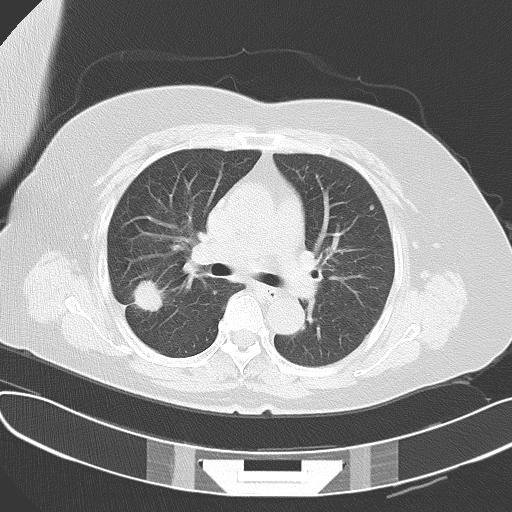
Chest CT, one axial slice; position 43 of 61 along the scan axis; 120 kVp; lung window (W 1500 / L -600 HU); 512 × 512 image matrix, field of view 367 × 367 mm. Patient: female, 63 years. Case-level facts recorded for this patient, not image findings: clinical TNM (as recorded): T1c N3 M1a.
Structures marked on this image (rectangle marked by the reading radiologist):
- lung tumour (recorded histology: adenocarcinoma): bounding box (x1, y1, x2, y2) in pixels: (131, 275, 165, 318)